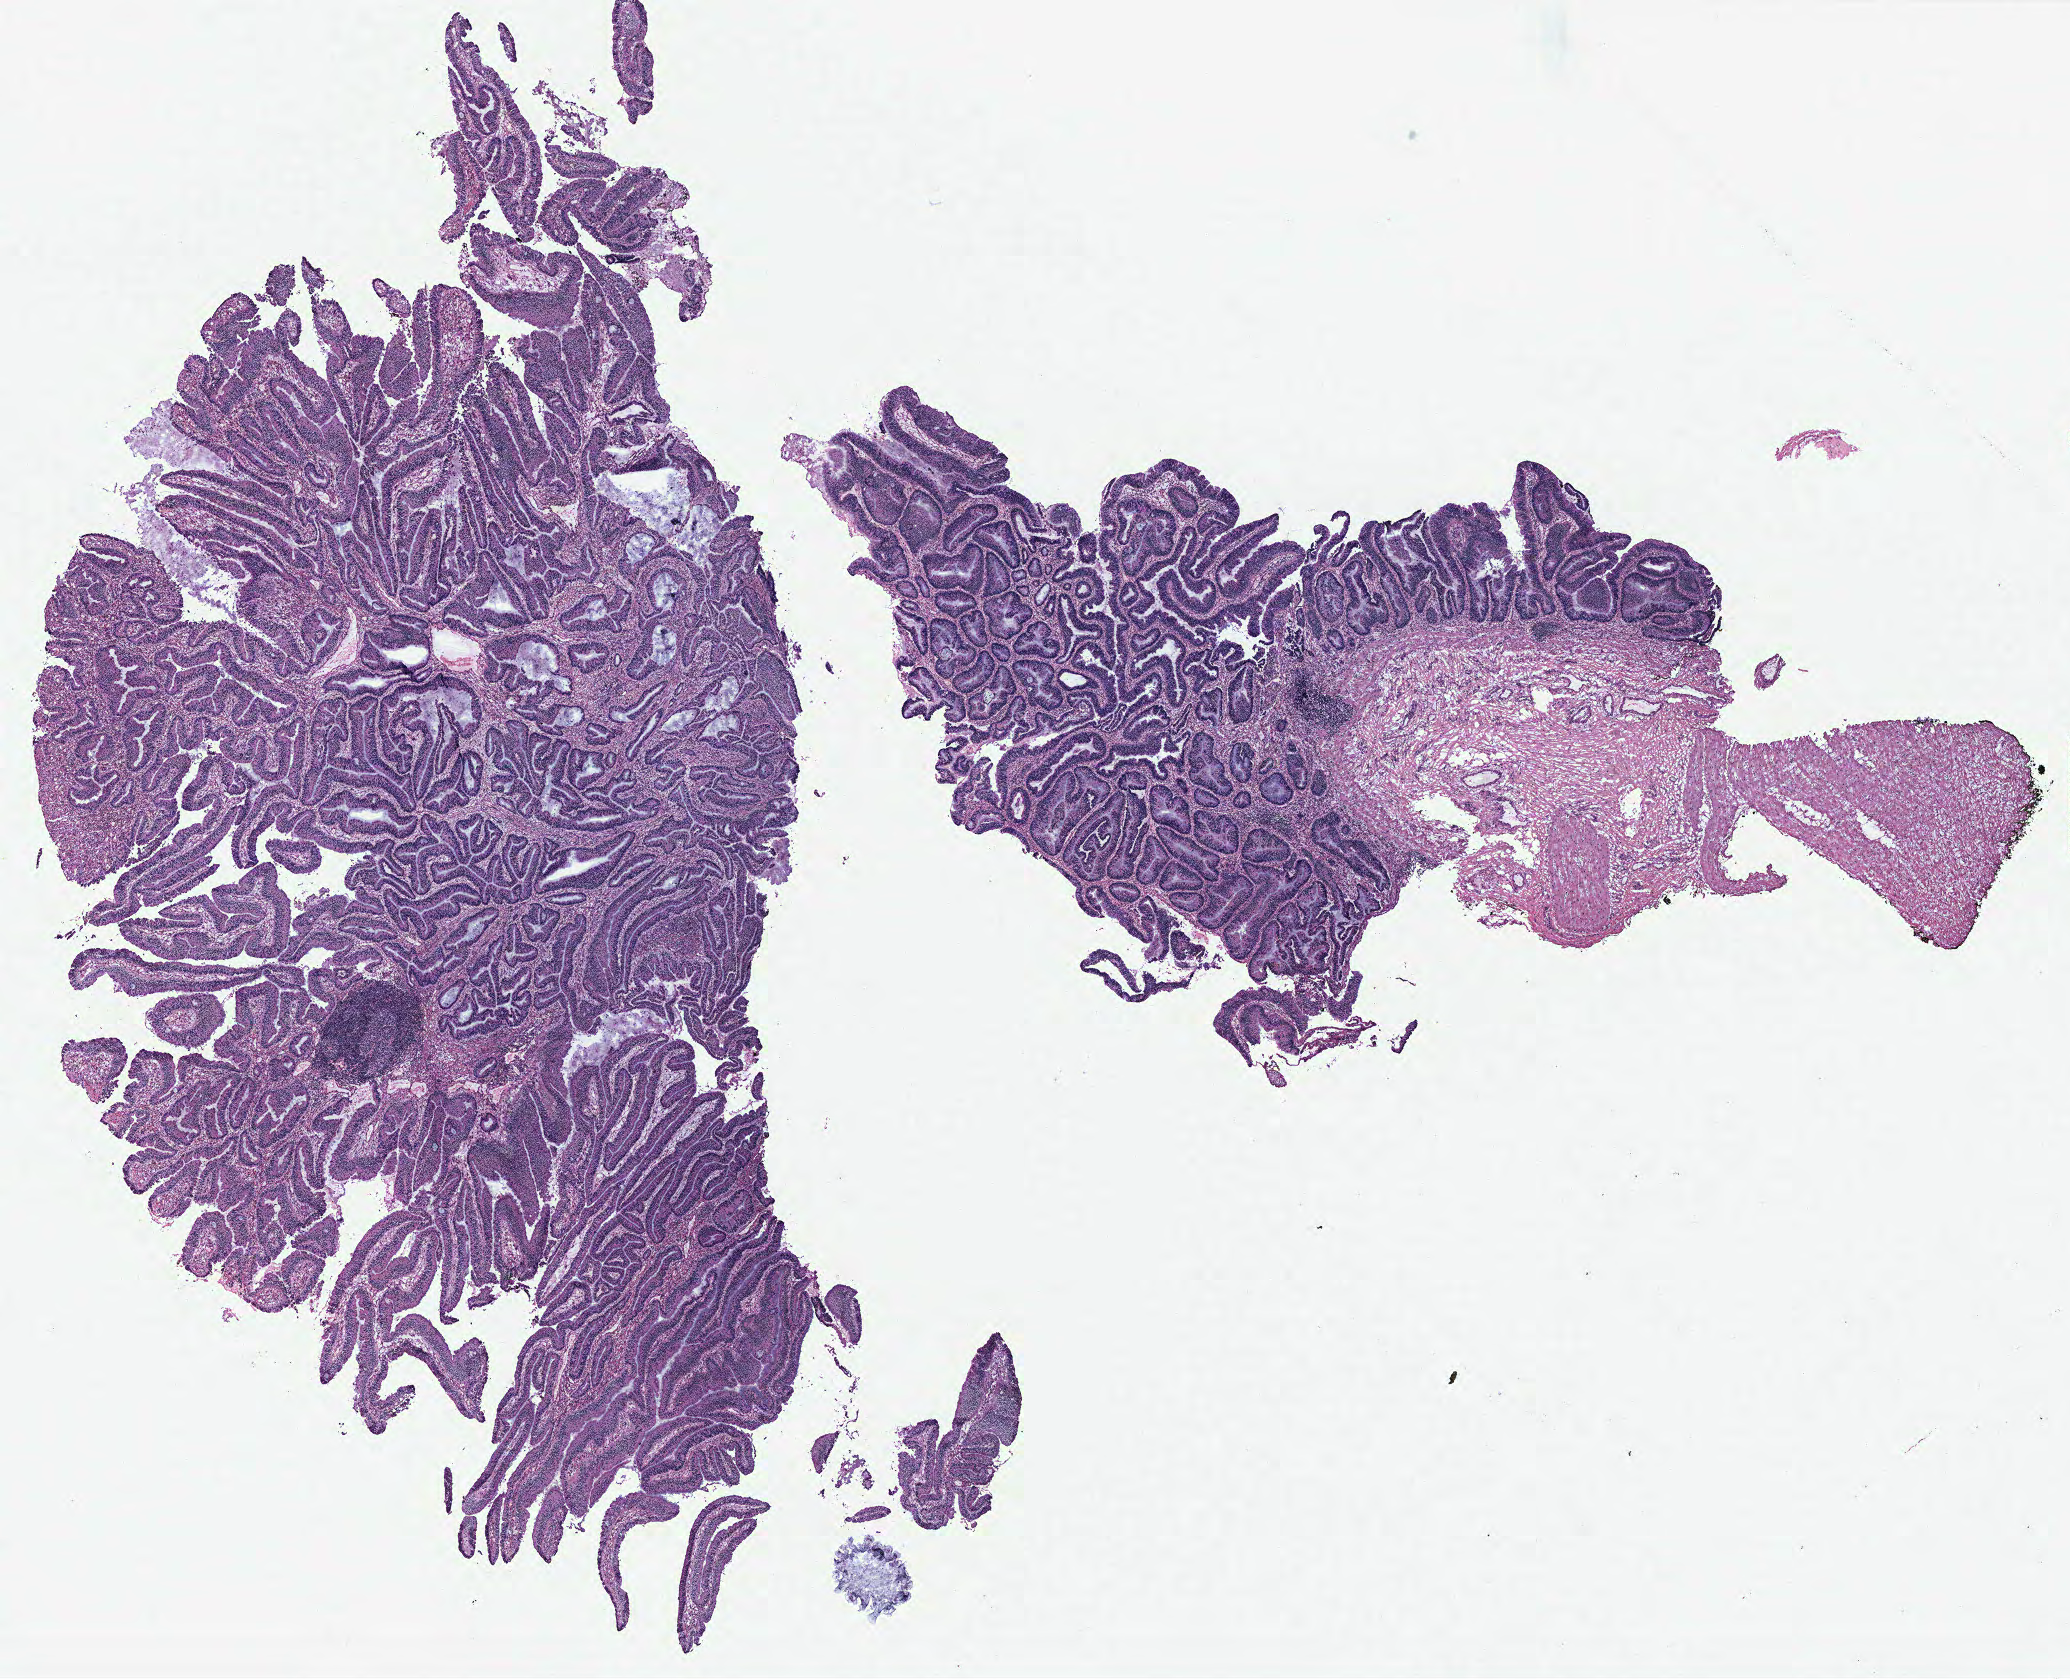
Whole-slide histology image, Hematoxylin and eosin (H&E) stained, a low-resolution overview of the entire scanned area, about 16.6 x 13.4 mm. Normal (non-tumour) tissue sample, colon. Female, 57 y/o.
This section: normal (non-tumour) tissue from the same patient. Patient diagnosis: Adenocarcinoma, NOS.